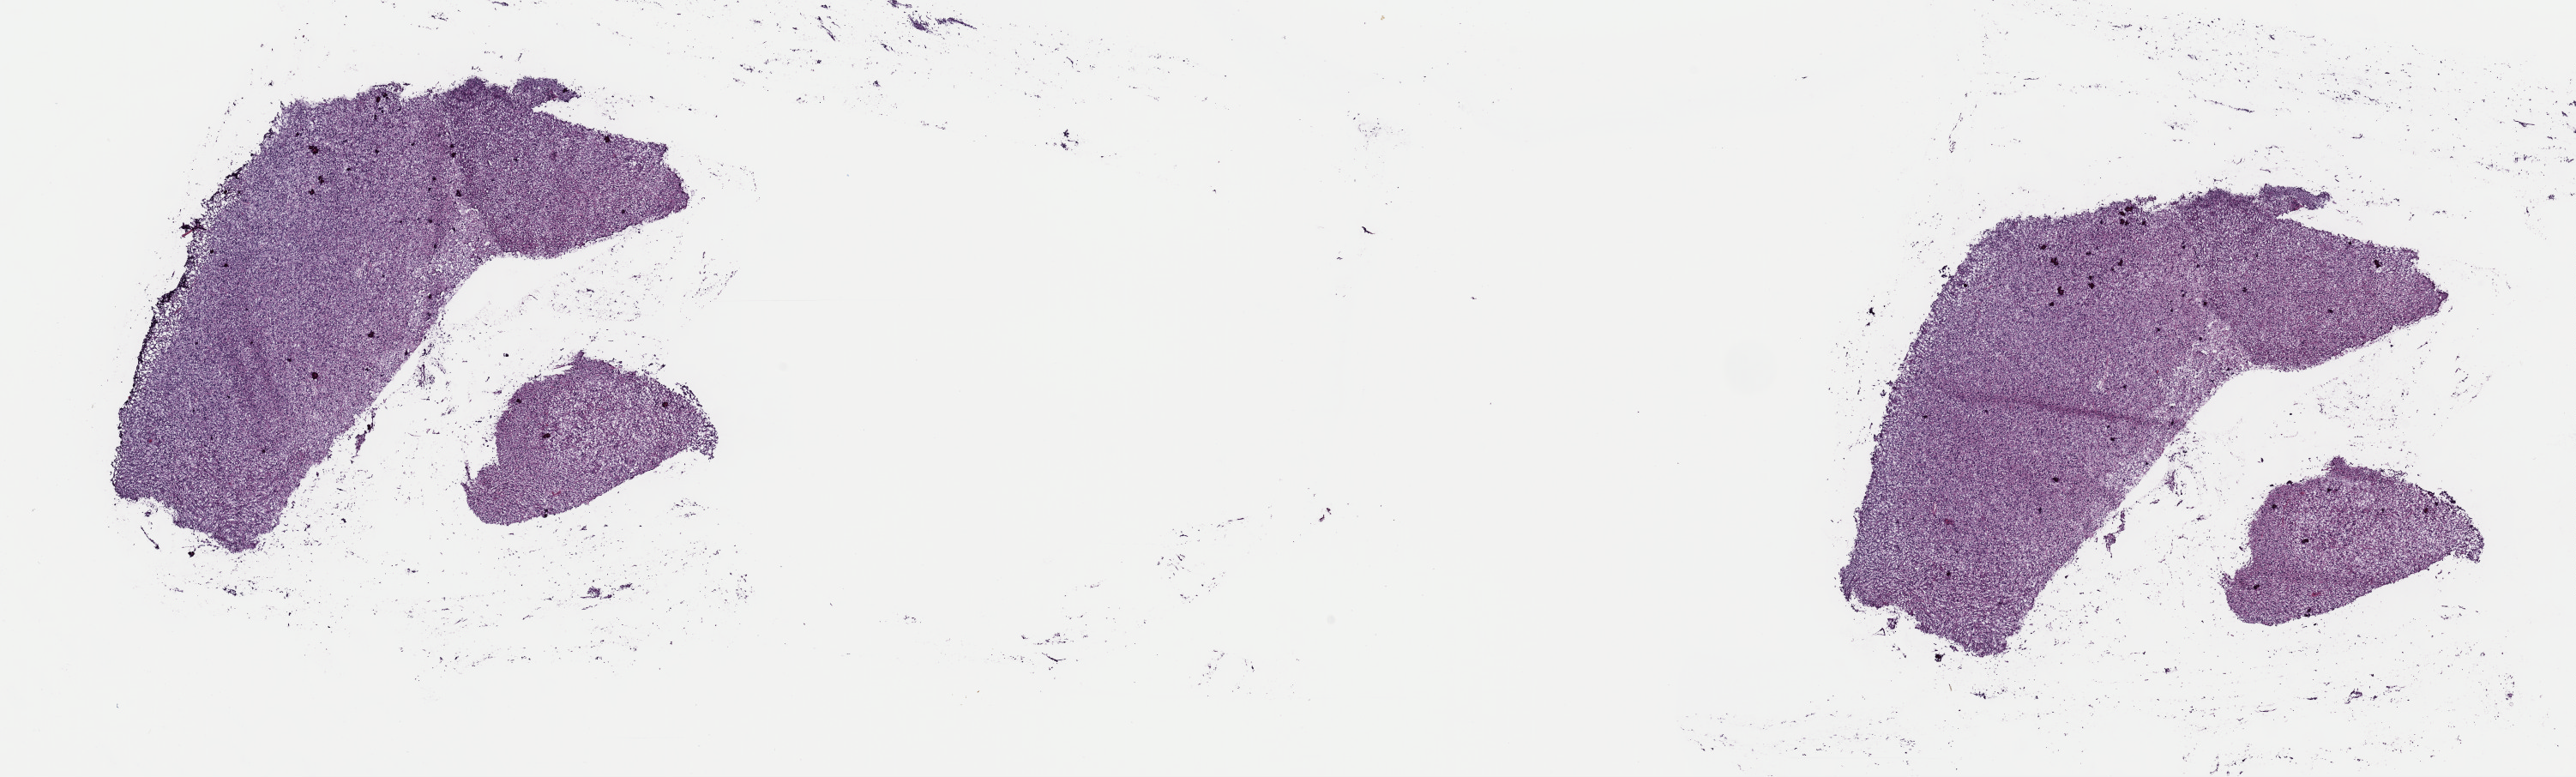
Whole-slide histology image, Hematoxylin and eosin (H&E) stained, whole scanned area (about 23.7 x 7.2 mm, from a 40x scan) shown as a low-resolution overview. Frozen section from the top of the tissue portion. Primary tumour sample from the brain. Female, age 21 years at initial diagnosis.
Pathologic diagnosis: Glioblastoma (occipital lobe).